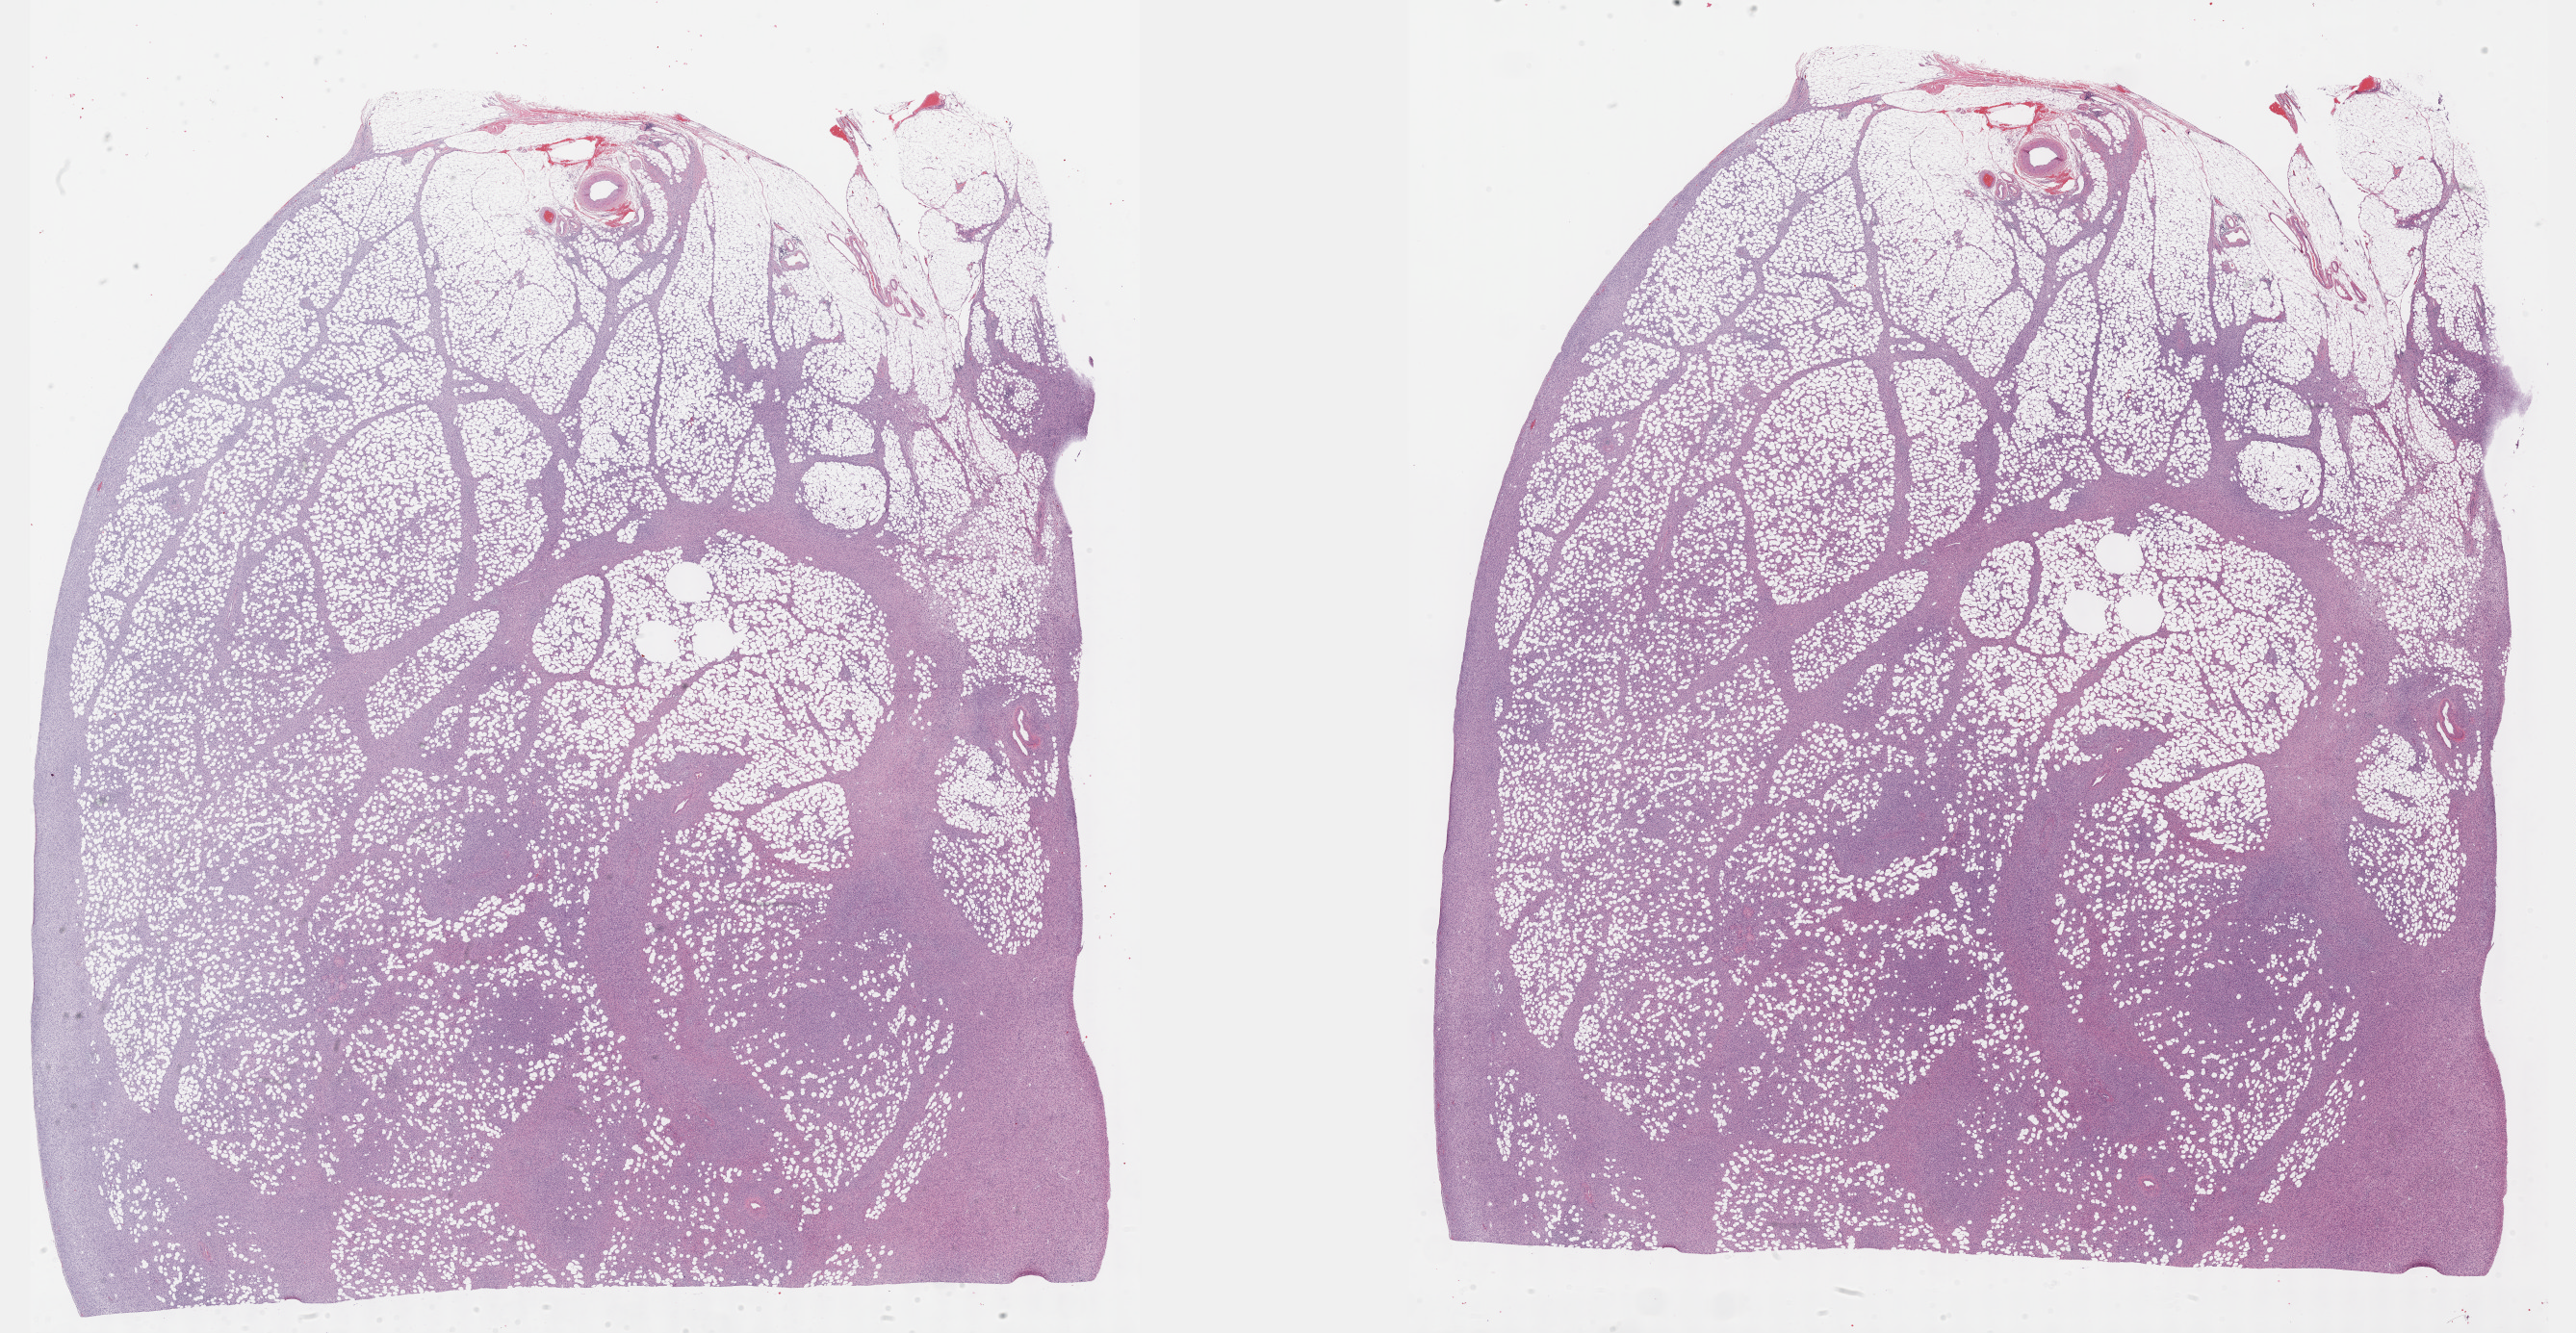
Digitized H&E-stained tissue section (whole slide), low-resolution overview of the scanned area, about 43.3 x 22.4 mm (acquisition: 40x scan). Formalin-fixed paraffin-embedded (FFPE) diagnostic section. Retroperitoneum and peritoneum, primary tumour sample. Female patient; age at initial diagnosis 60 years.
* histologic diagnosis: Dedifferentiated liposarcoma (retroperitoneum)